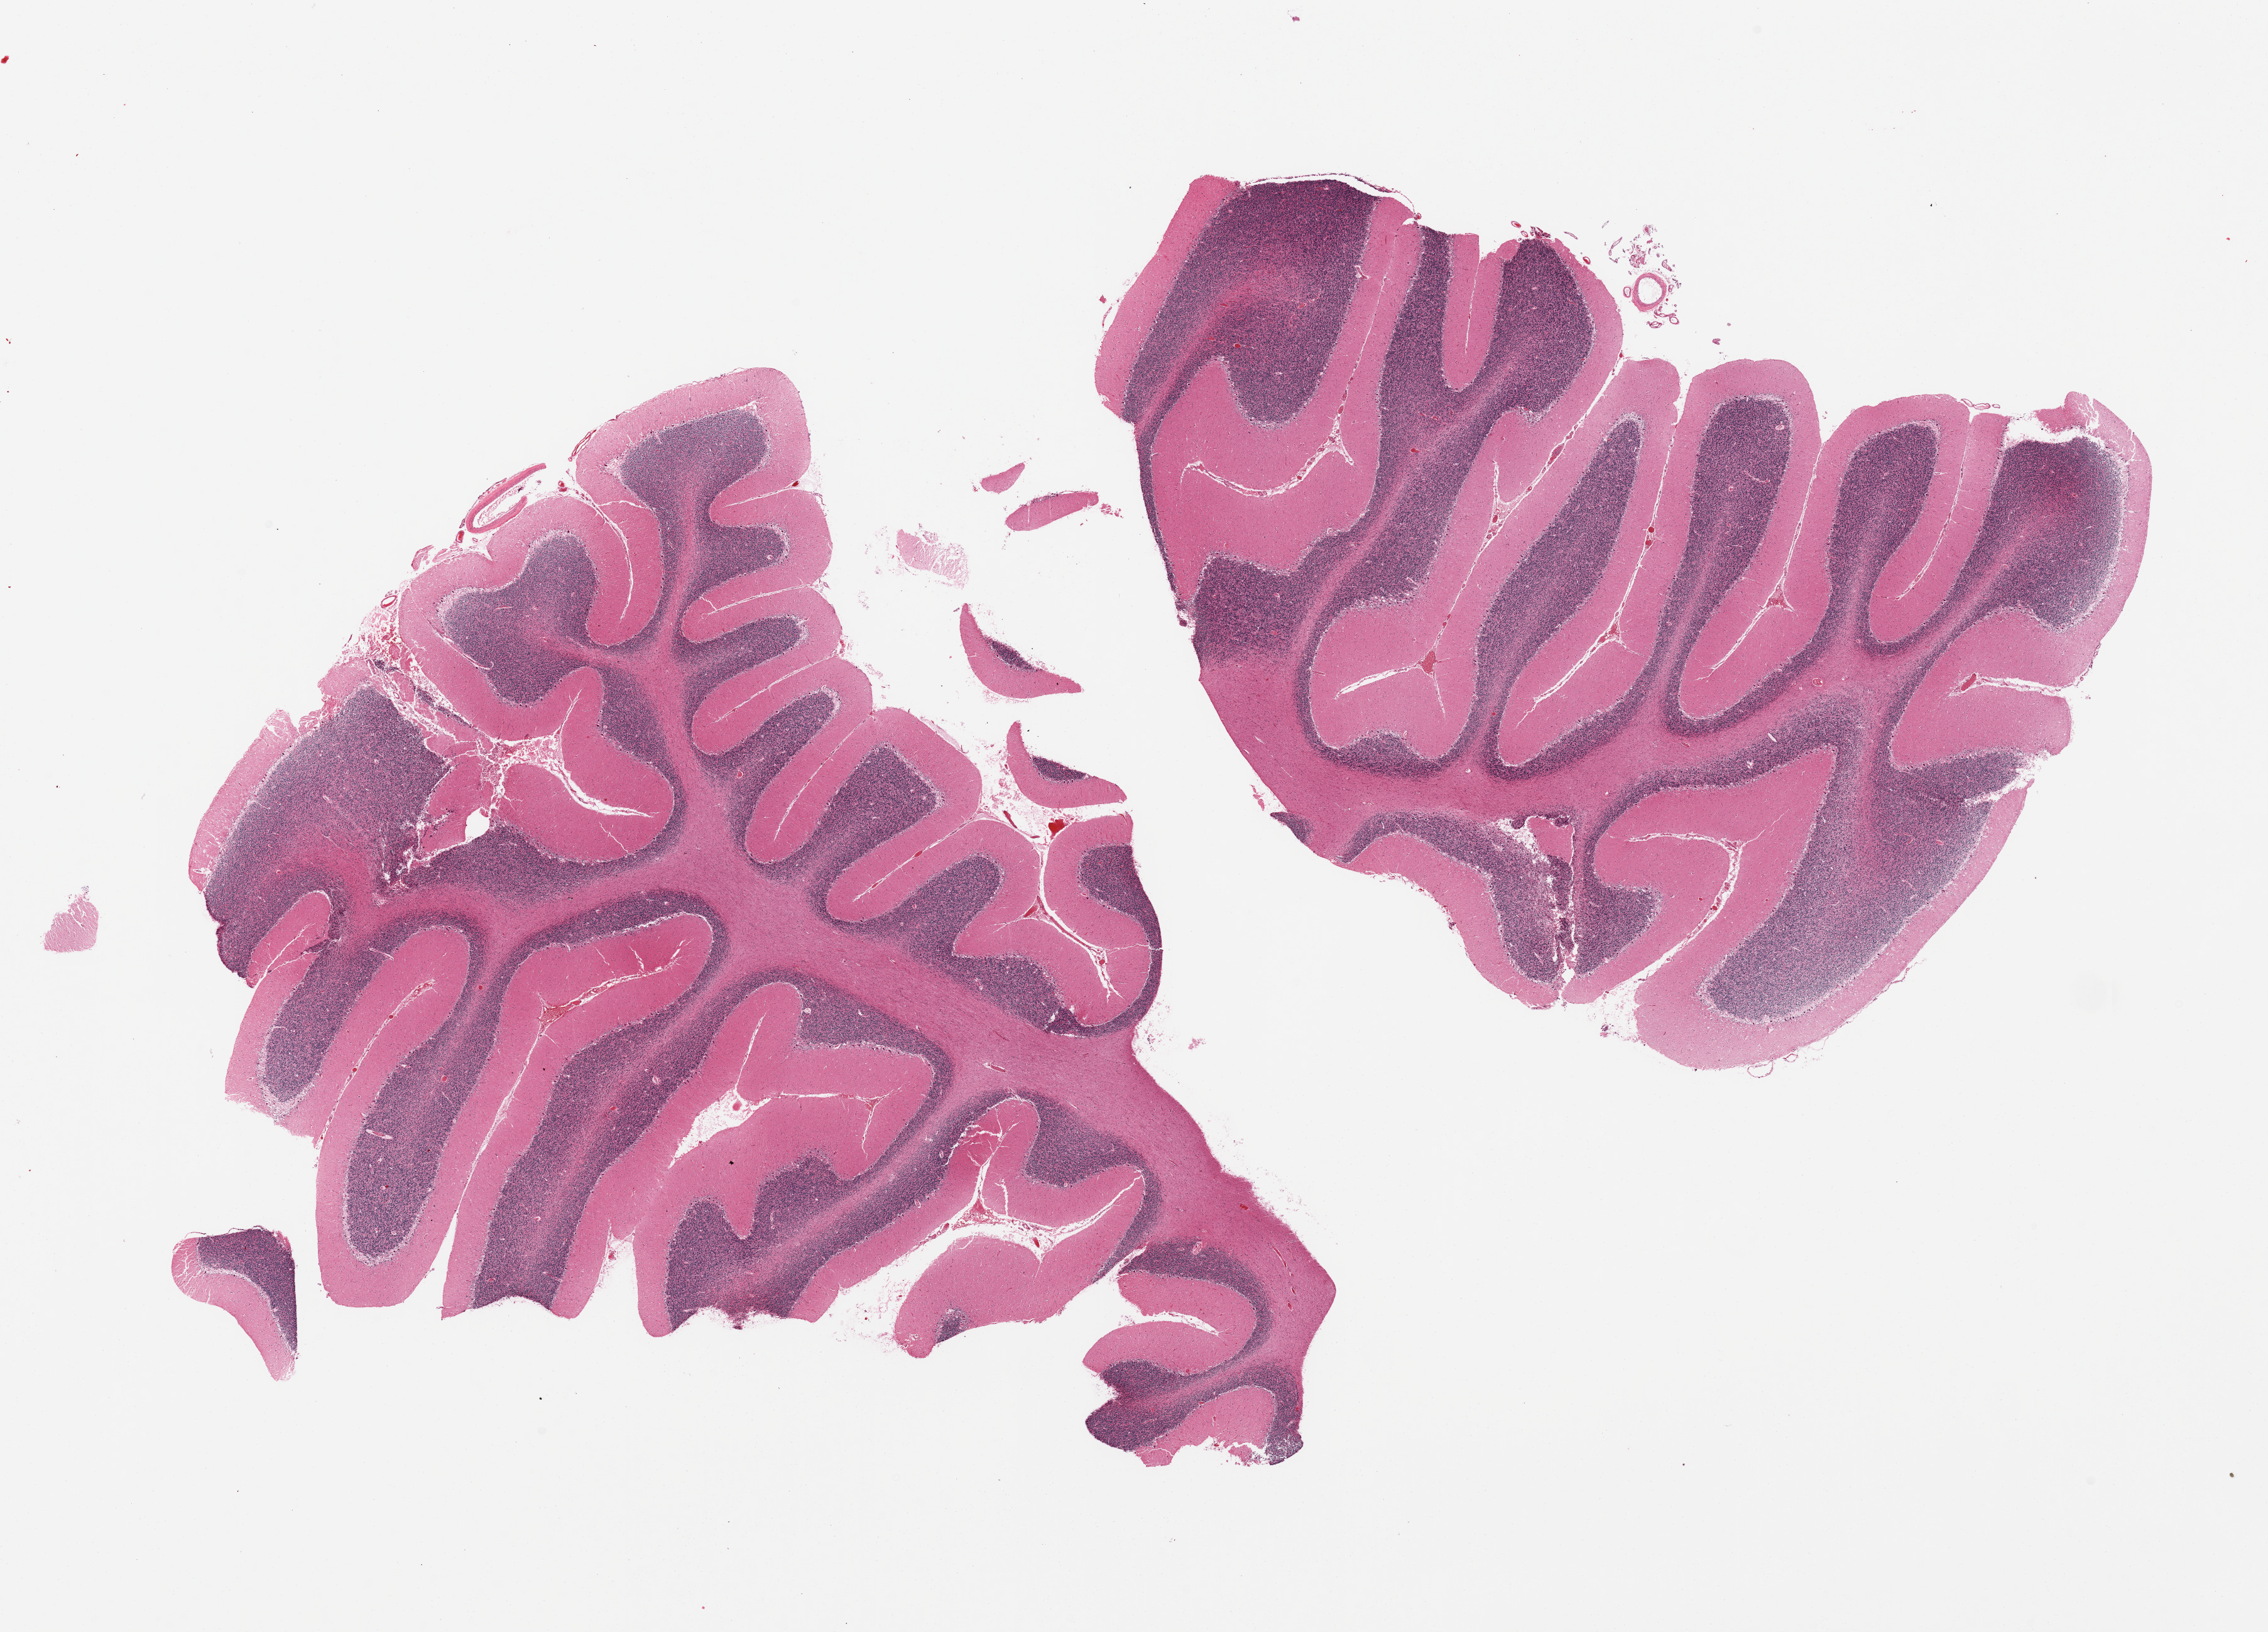
Whole-slide image, haematoxylin and eosin stain, whole scanned area (about 28.5 x 20.5 mm, acquisition: 20x scan) shown as a low-resolution overview, PAXgene-fixed paraffin-embedded (PFPE) section, target tissue: cerebellum, donor tissue sample. Female donor.
• pathologist's review note for this sample: 2 pieces